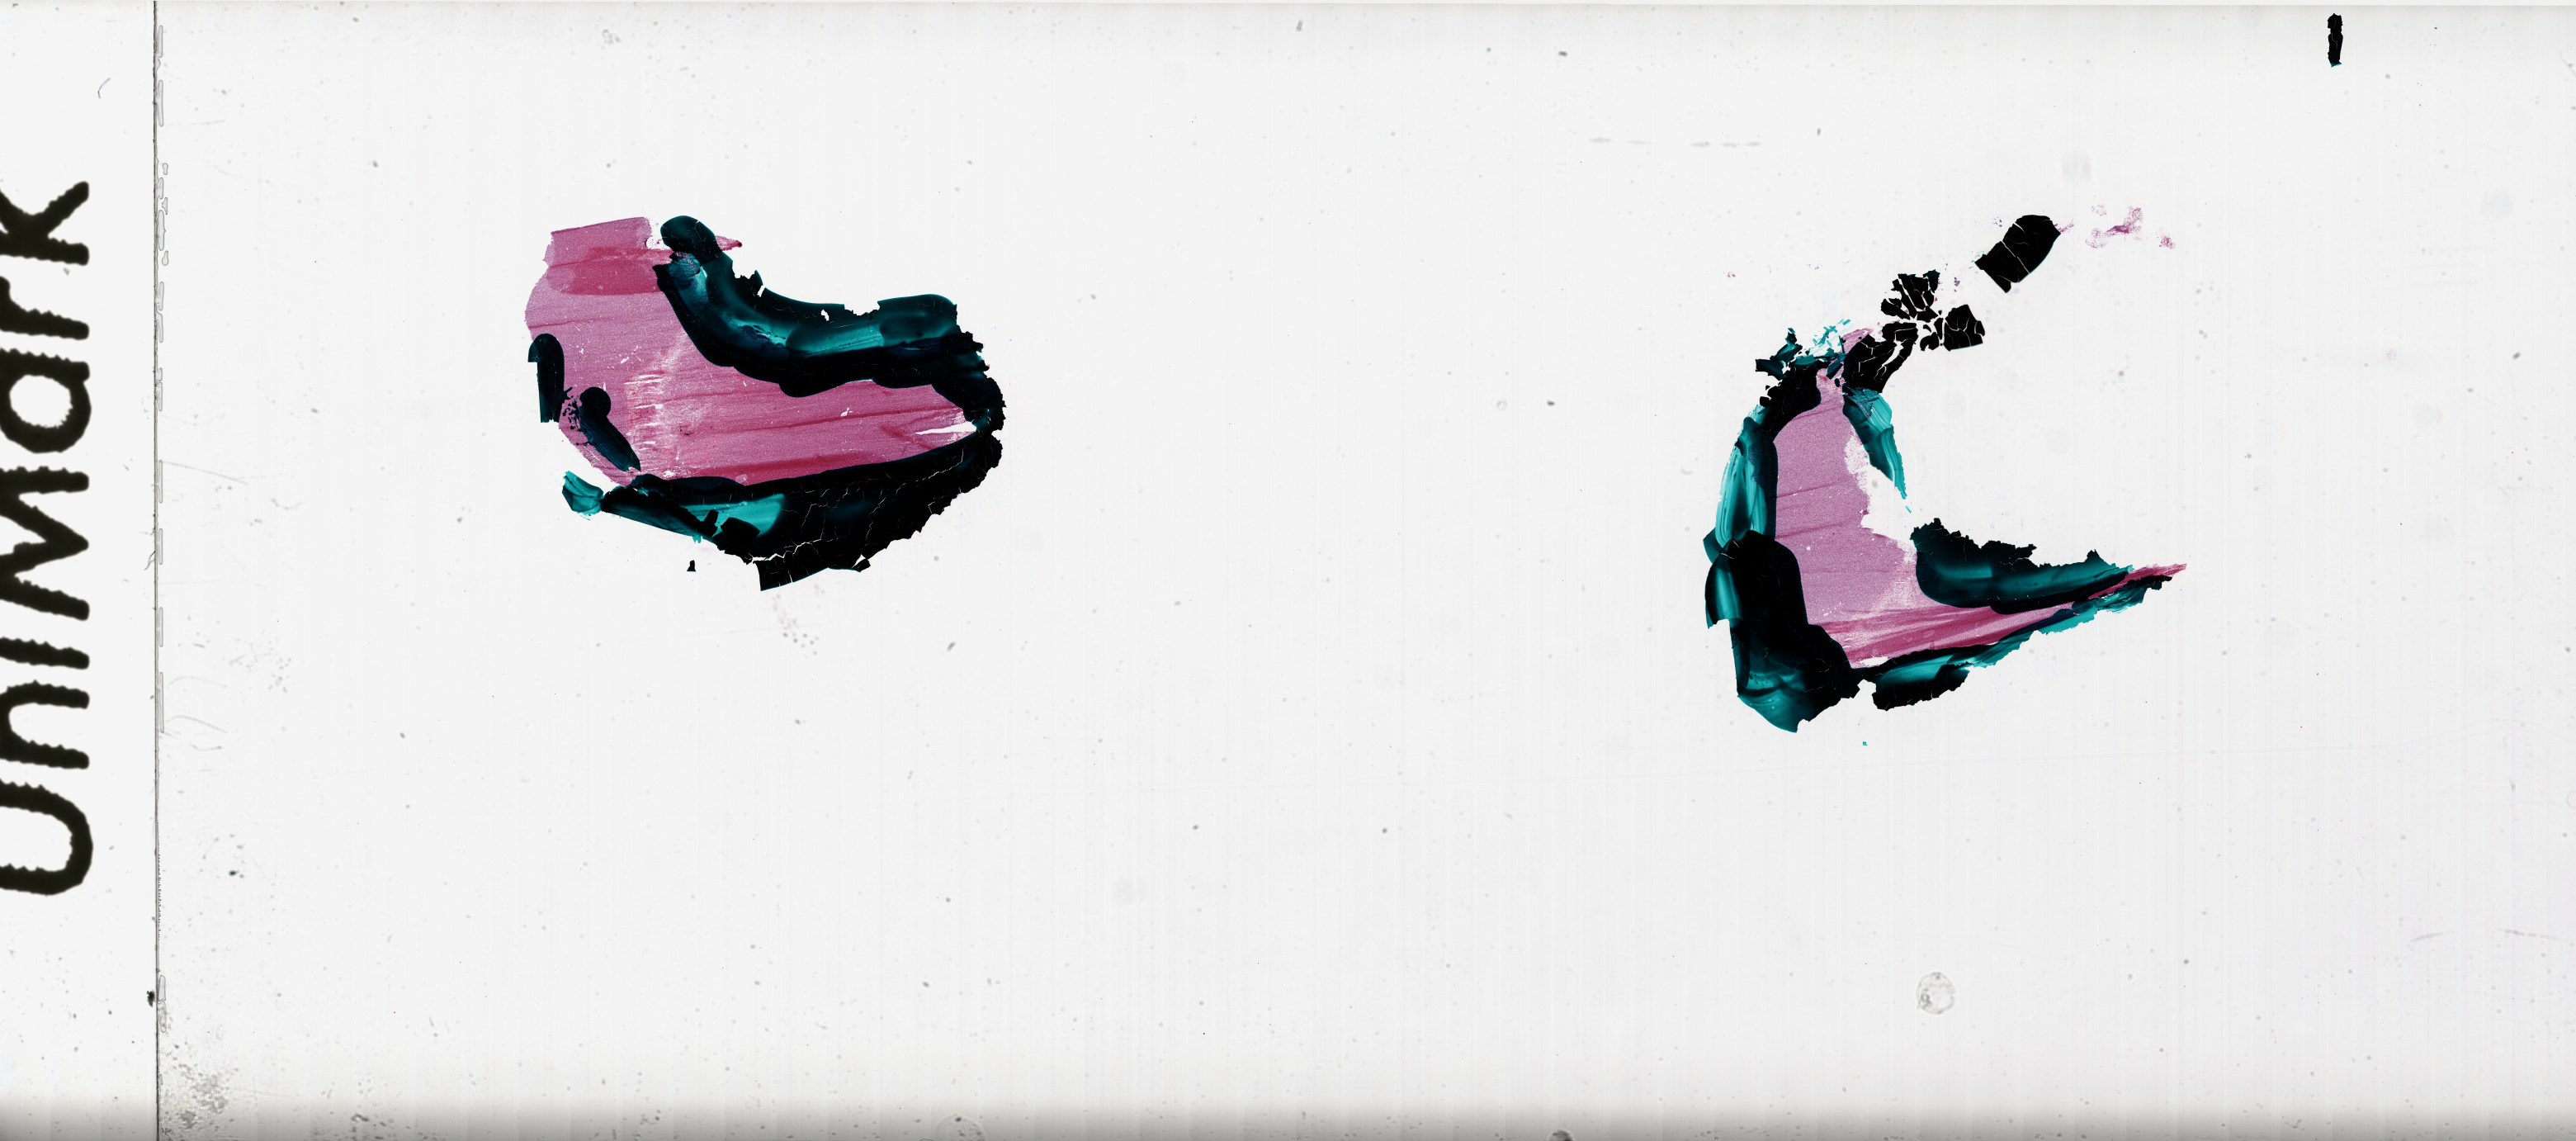
Digitized H&E-stained tissue section (whole slide), whole scanned area (about 49.9 x 22.1 mm) shown as a low-resolution overview. Frozen section. Primary tumour sample from the brain. Female patient; age at initial diagnosis 53 years. Slide review estimates, as recorded: tumour cells 90%, tumour nuclei 100%, normal cells 0%, stromal cells 0%, necrosis 10%. Infiltration values recorded for this section: lymphocyte infiltration 0%, monocyte infiltration 0%, neutrophil infiltration 0%.
Diagnosis: Glioblastoma.